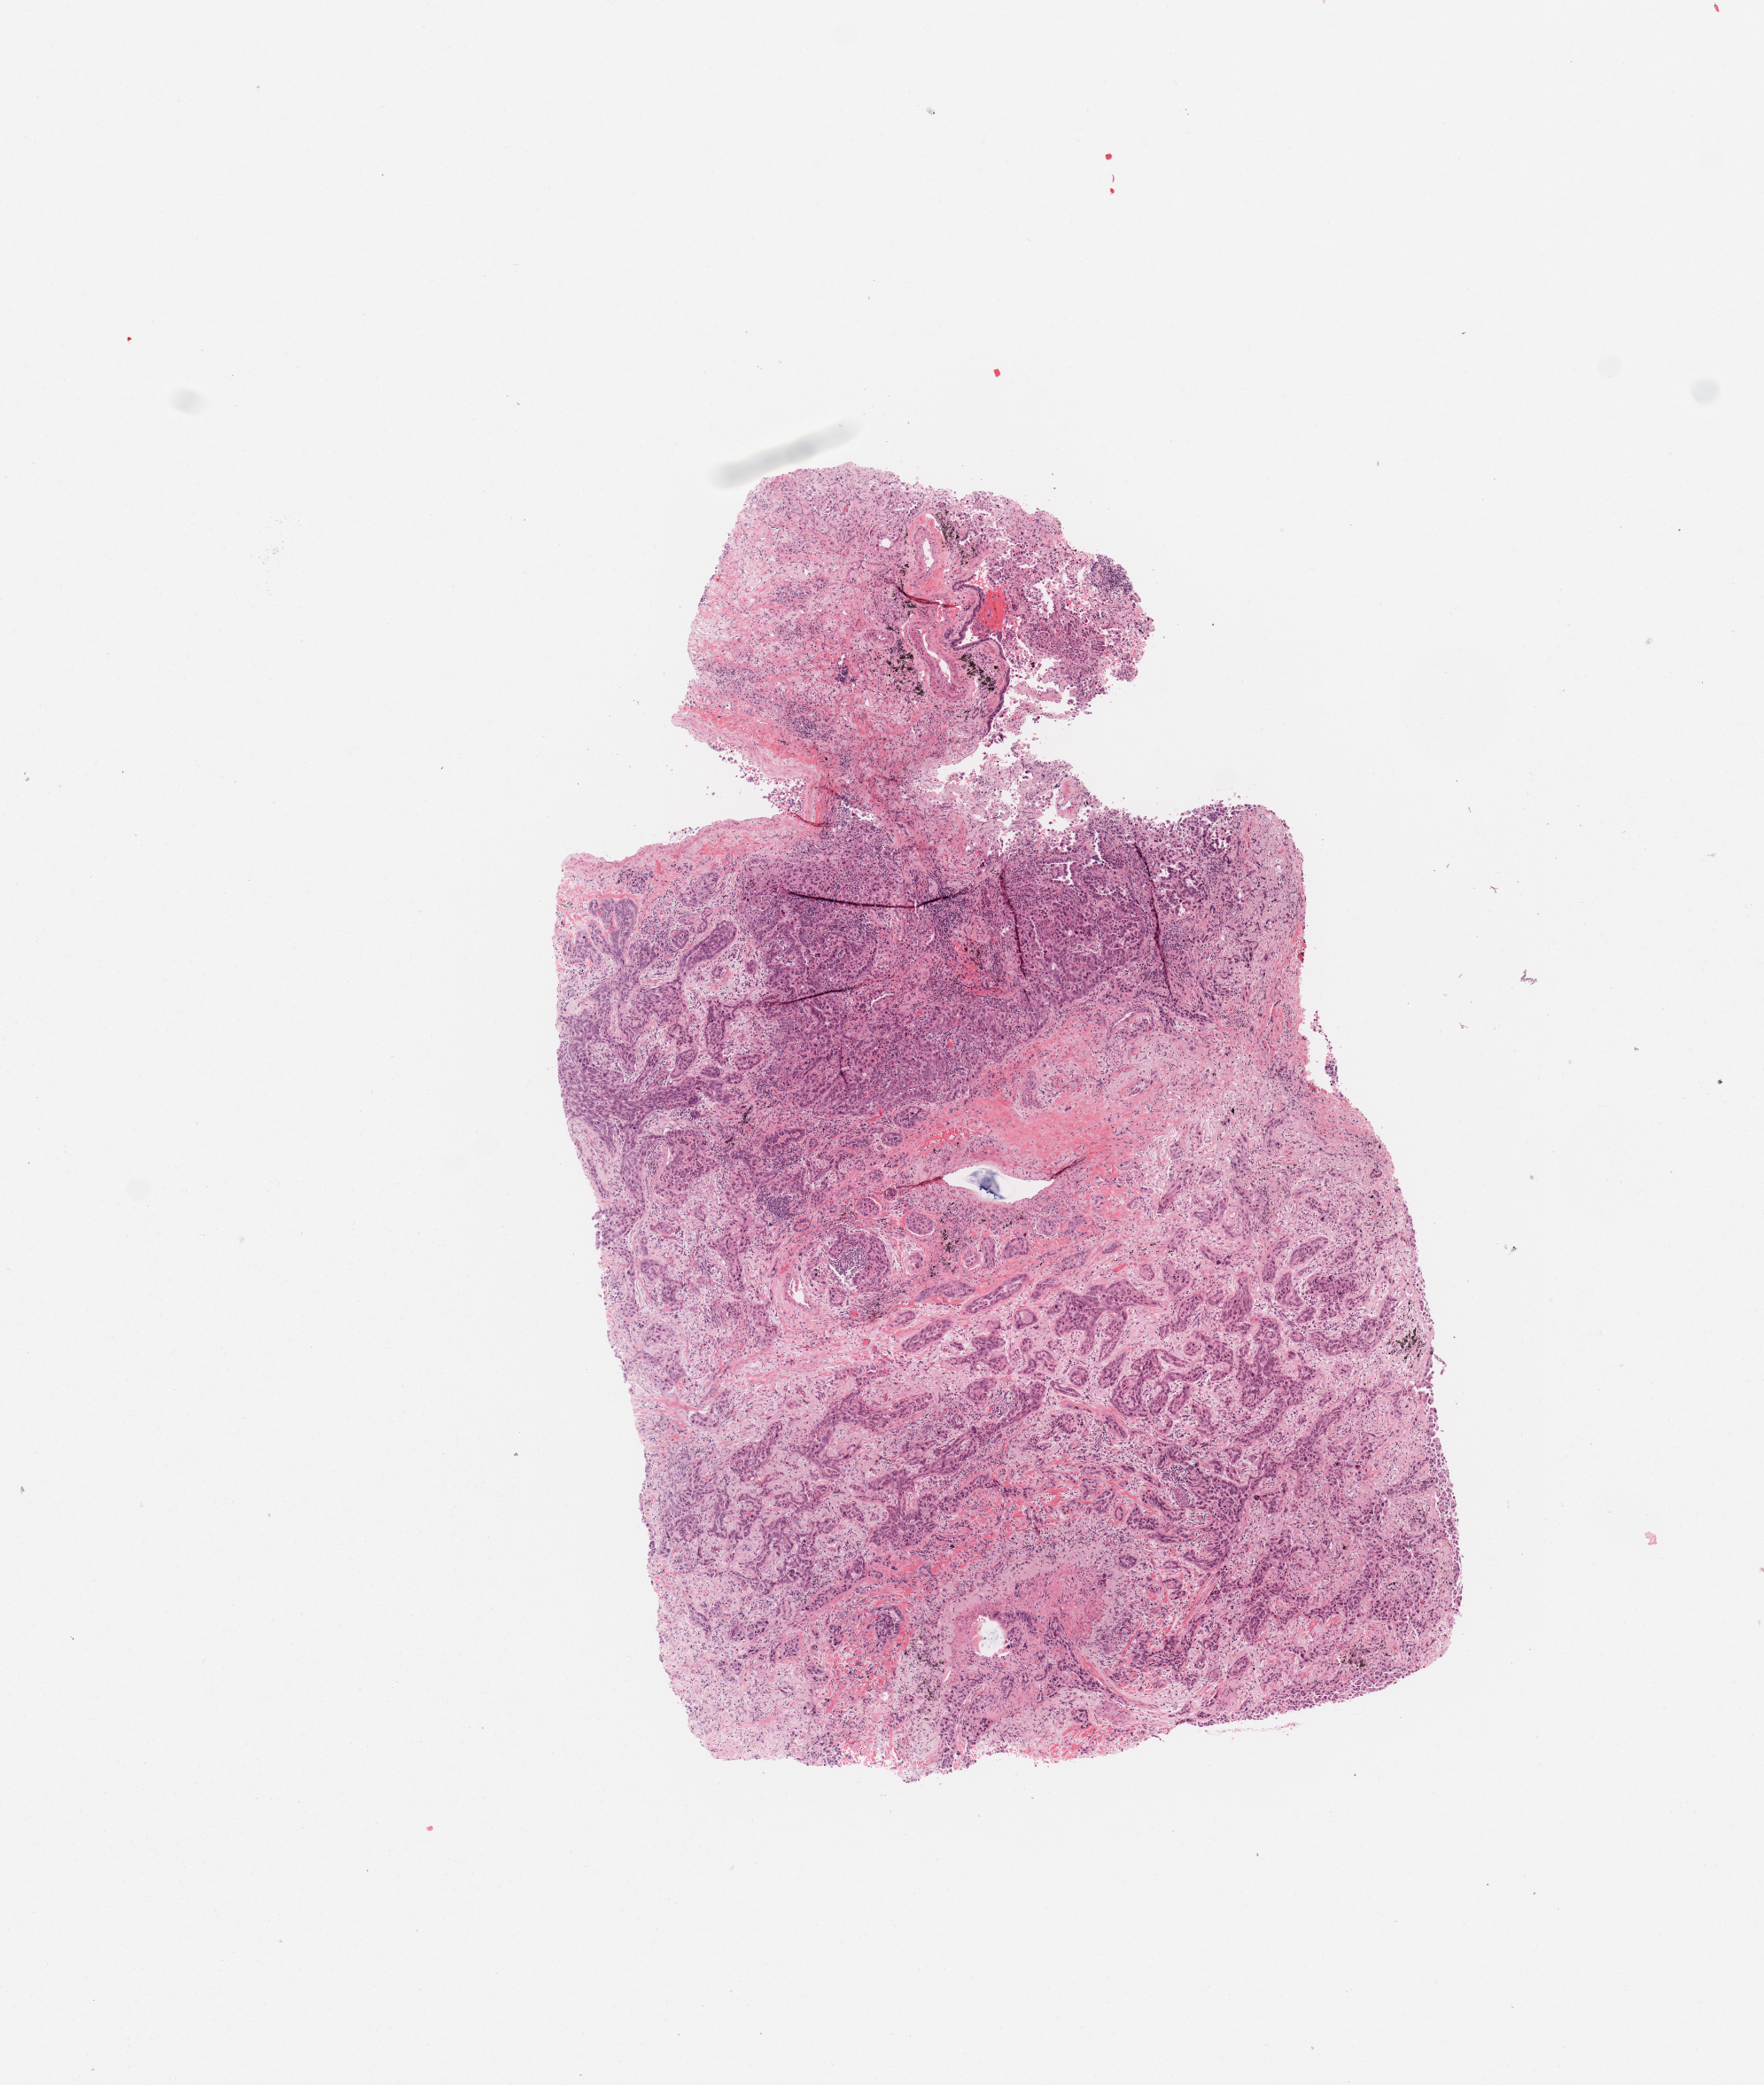
Whole-slide histology image, H&E, shown as a low-resolution overview of the whole scanned area (about 7.9 x 9.3 mm), tumour tissue sample, sampled site: lung. Patient: male, age 61 years. Histologic grade: G2 (moderately differentiated). Composition of this section per pathologist review: tumour nuclei 70%, necrosis 3%.
Histologic diagnosis: Adenocarcinoma, NOS. AJCC pathologic stage: IIB.